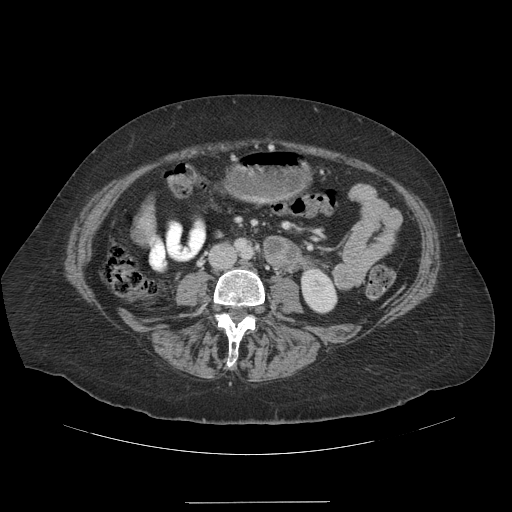
Contrast-enhanced abdominal CT (liver protocol), one axial slice. Position 27 of 99 along the scan axis. Reconstruction kernel STANDARD. Soft-tissue window (W 400 / L 40 HU). 512 × 512 image matrix, field of view 440 × 440 mm. Case-level facts recorded for this patient, not image findings: diagnosis: hepatocellular carcinoma (patient treated with transarterial chemoembolisation; whether this scan precedes or follows treatment is not stated here); TNM stage (as recorded): Stage-IVA; Child-Pugh class: A; tumour nodularity: multinodular.
Outlined on this slice (semi-automatic segmentation, software-assisted and operator-edited):
- liver parenchyma outside the tumour (the mass and vessels are separate outlines, so this box may not span the whole liver): box from (x=140, y=214) to (x=154, y=234) px